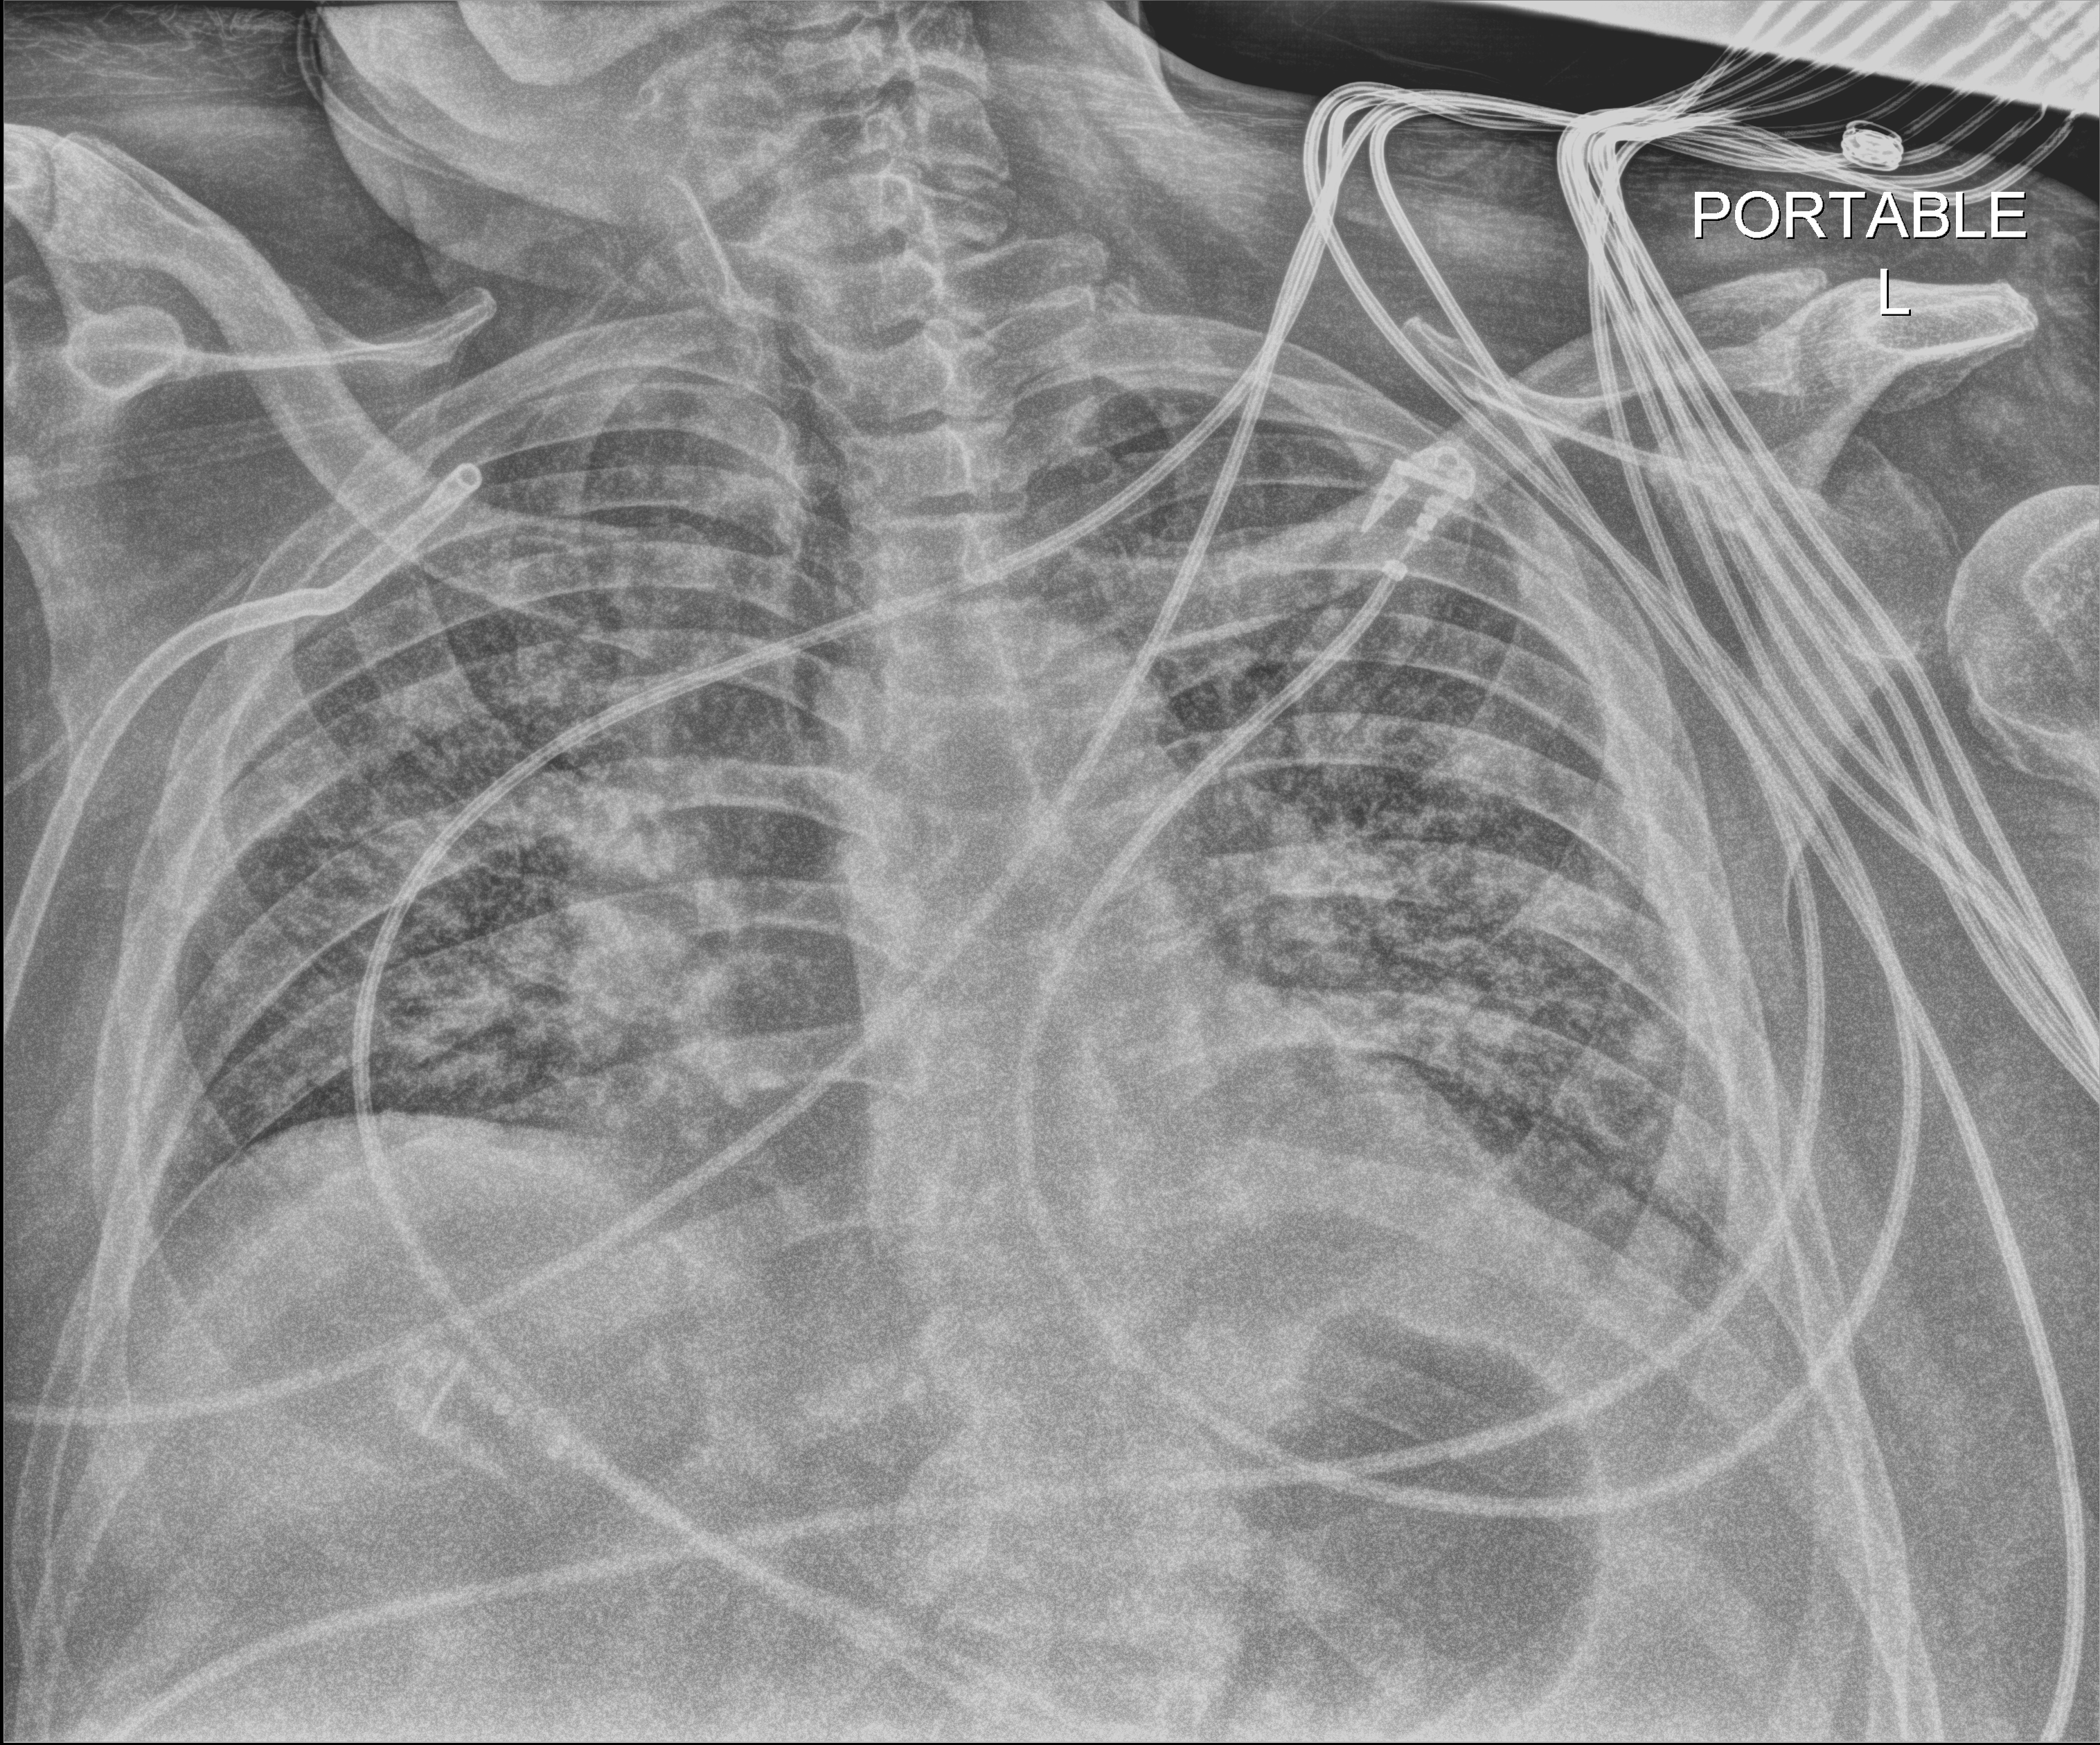
Chest radiograph, anteroposterior (AP) projection. Patient hospitalised with COVID-19; male, aged 60–74 years.
From the hospital-stay record, not from the radiograph (when in the stay this image was taken is not recorded): length of hospital stay: 34 days.